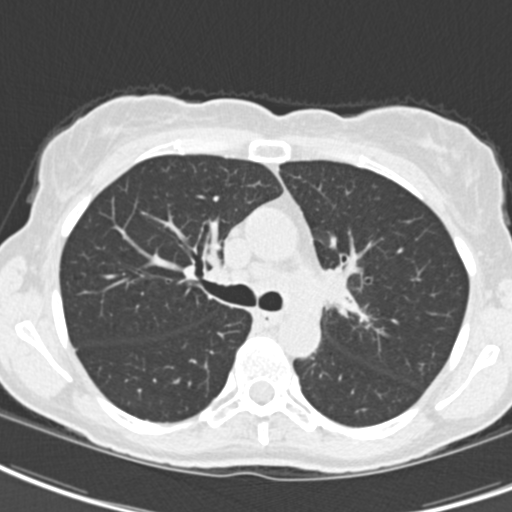
Low-dose screening chest CT, one axial slice. Slice 131 of 189 in the series (ordered by position). Reconstruction kernel B30f. 120 kVp. Lung window (W 1500 / L -600 HU). 2 mm slice thickness. 512 × 512 image matrix, field of view 279 × 279 mm.
Annotated regions visible in this slice (outlined manually by an expert reader):
- lesion 2 (tumor, hilum of left lung): bounding box <321,265,350,306> (left, top, right, bottom; pixels)